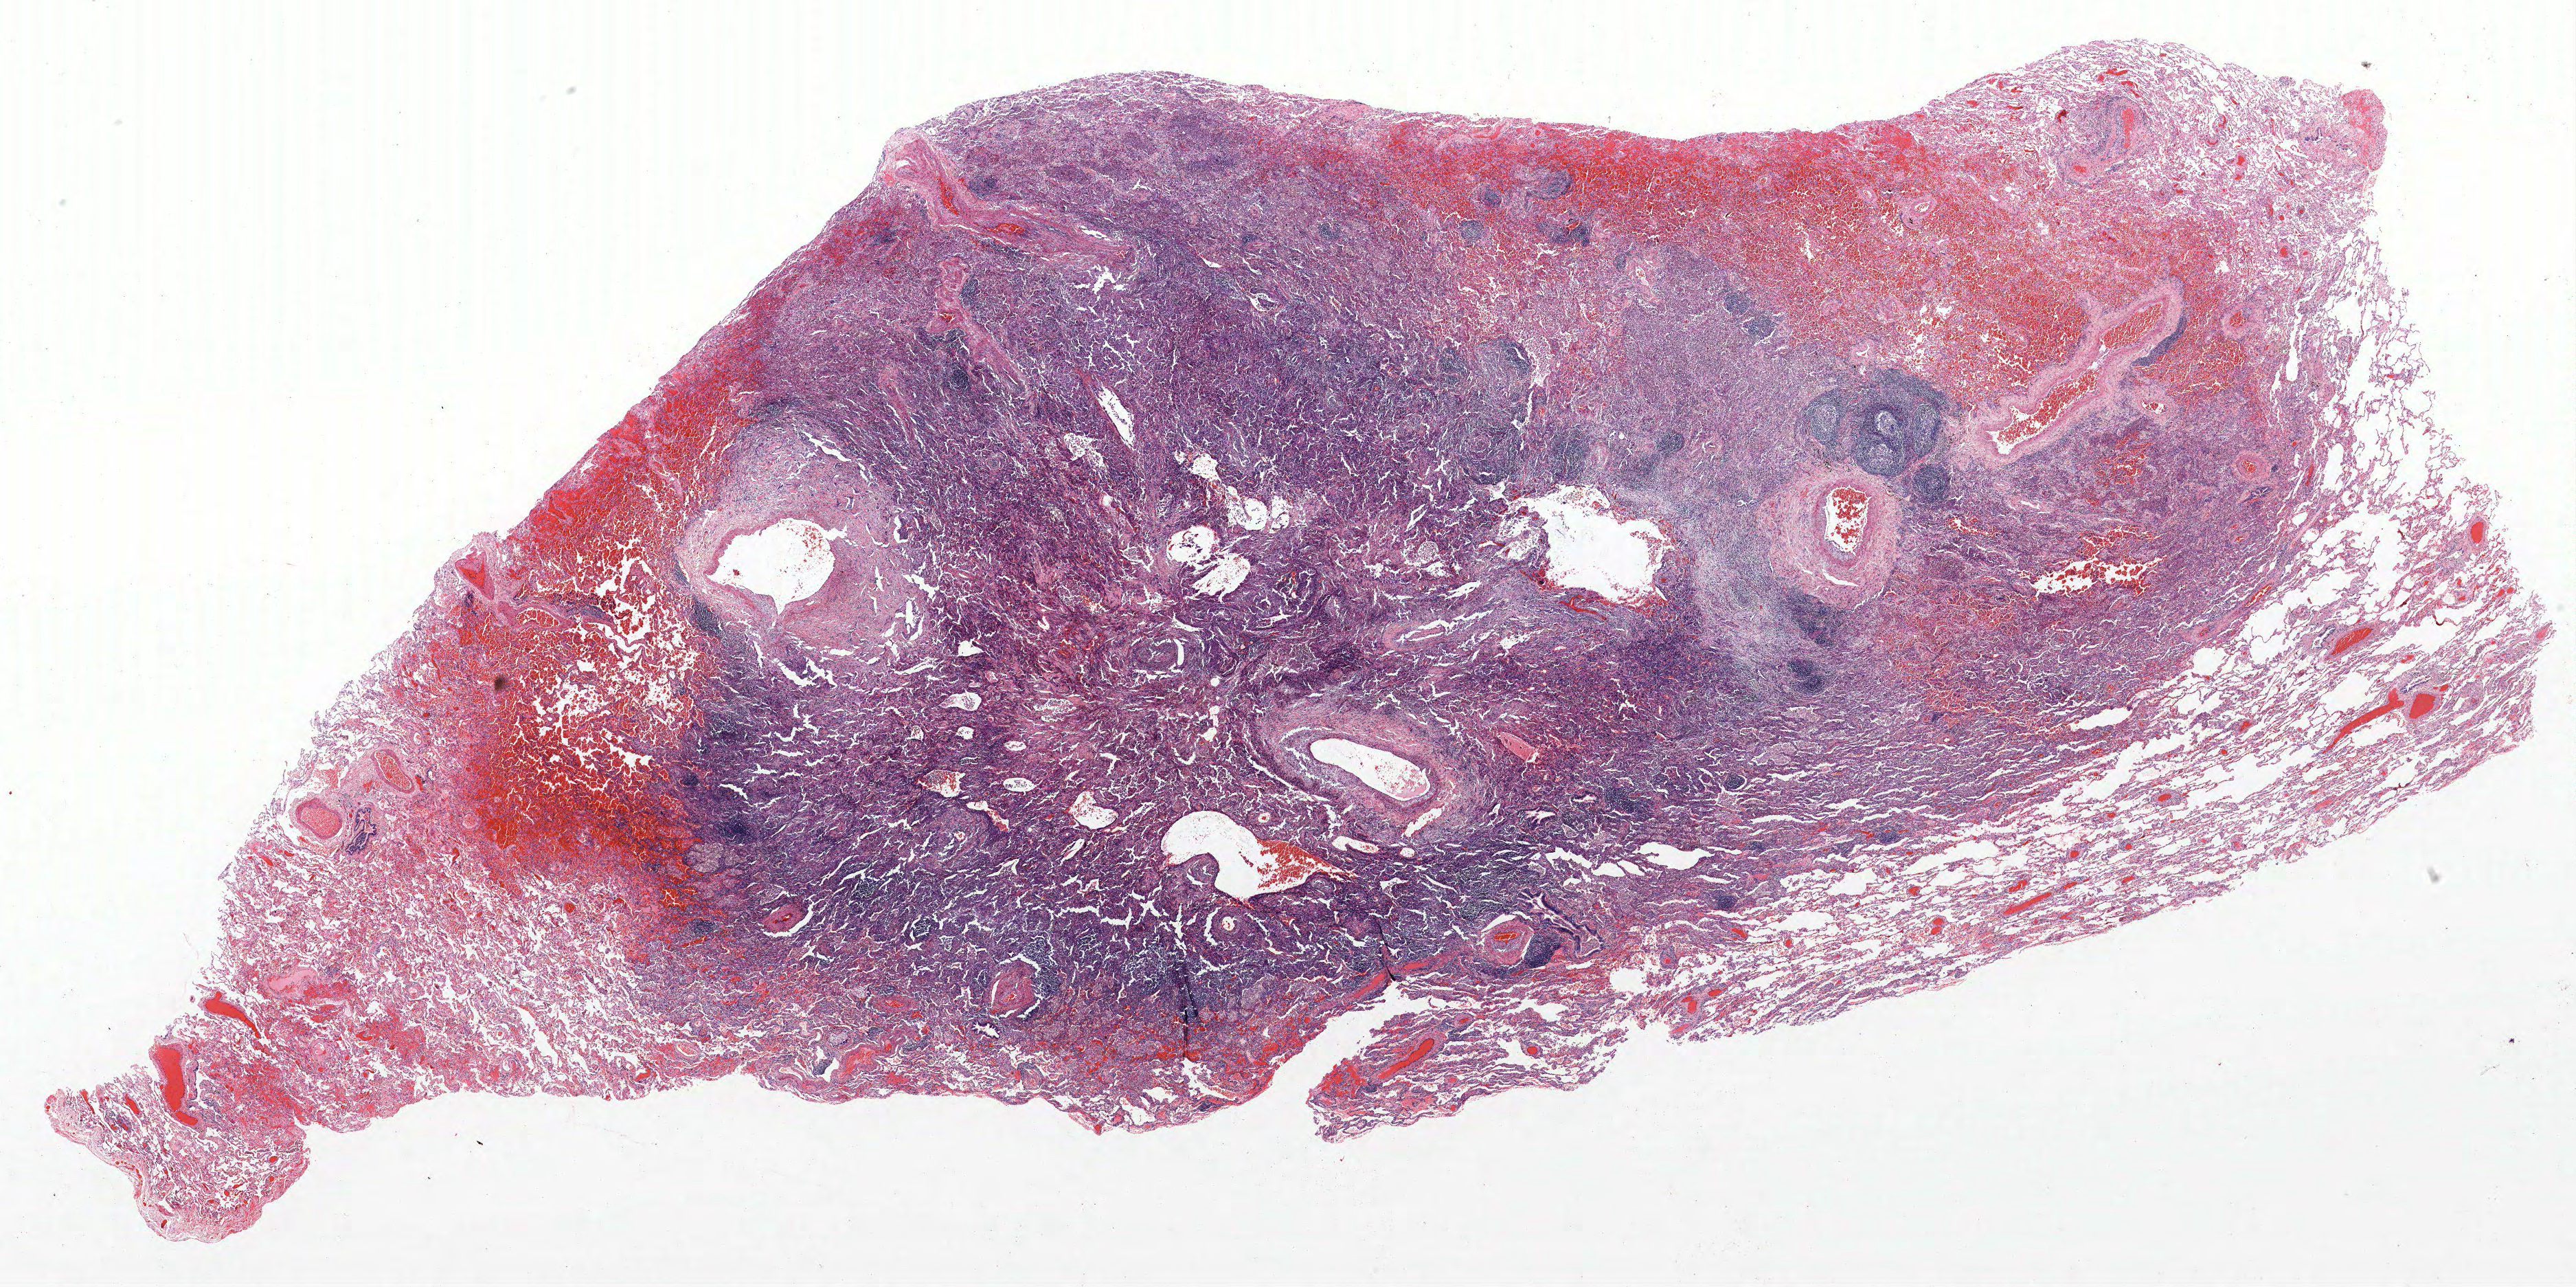
H&E-stained whole-slide image, low-resolution overview of the scanned area, about 30.0 x 15.0 mm (slide scanned at 40x), formalin-fixed paraffin-embedded (FFPE) section, lung tissue. Male, age 57 at enrolment. Current smoker at enrolment. Grade: poorly differentiated (G3).
Tumour size (pathology): 15 mm. Primary tumour location (clinical record): left upper lobe. Stage (AJCC 6th edition): IA. Participant's lung-cancer diagnosis: Adenosquamous carcinoma.